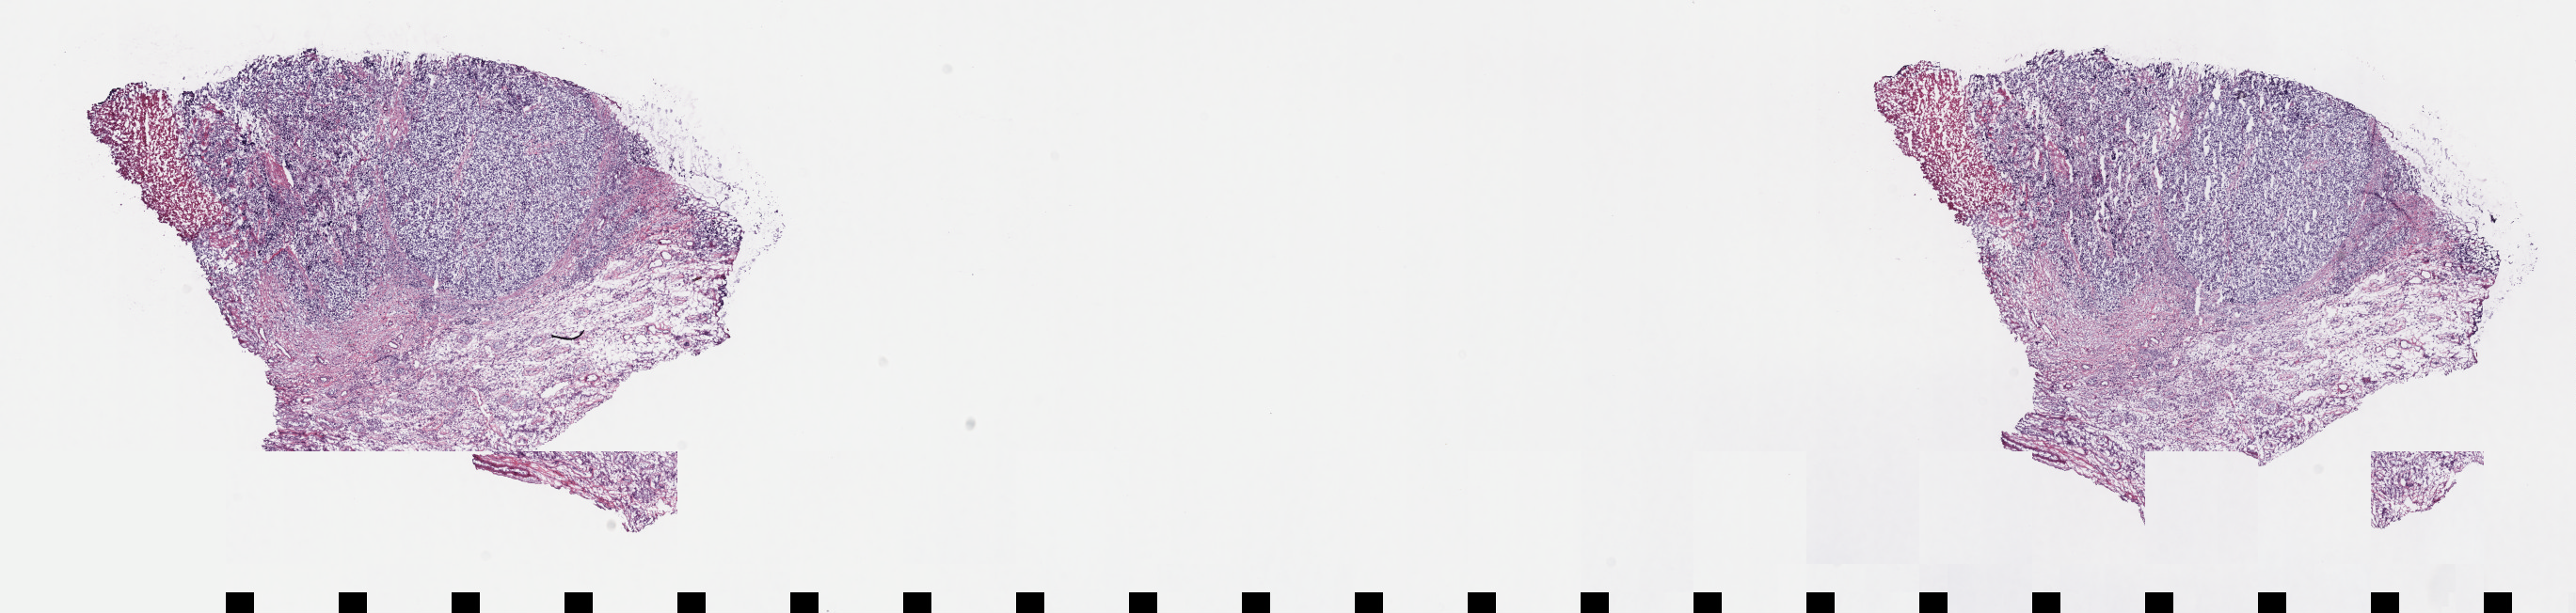
Whole-slide histology image, Hematoxylin and eosin (H&E) stained — a low-resolution overview of the entire scanned area, about 22.1 x 5.3 mm (acquisition: 40x scan), frozen section from the top of the tissue portion, sample: primary tumour, testis. Male, age 31 years at initial diagnosis. Slide review estimates, as recorded: tumour cells 70%, tumour nuclei 70%, normal cells 0%, stromal cells 25%, necrosis 5%. Inflammatory infiltration, as recorded: lymphocyte infiltration 40%, monocyte infiltration 20%, neutrophil infiltration 20%.
• AJCC pathologic stage: IS (7th edition)
• histologic diagnosis: Seminoma, NOS